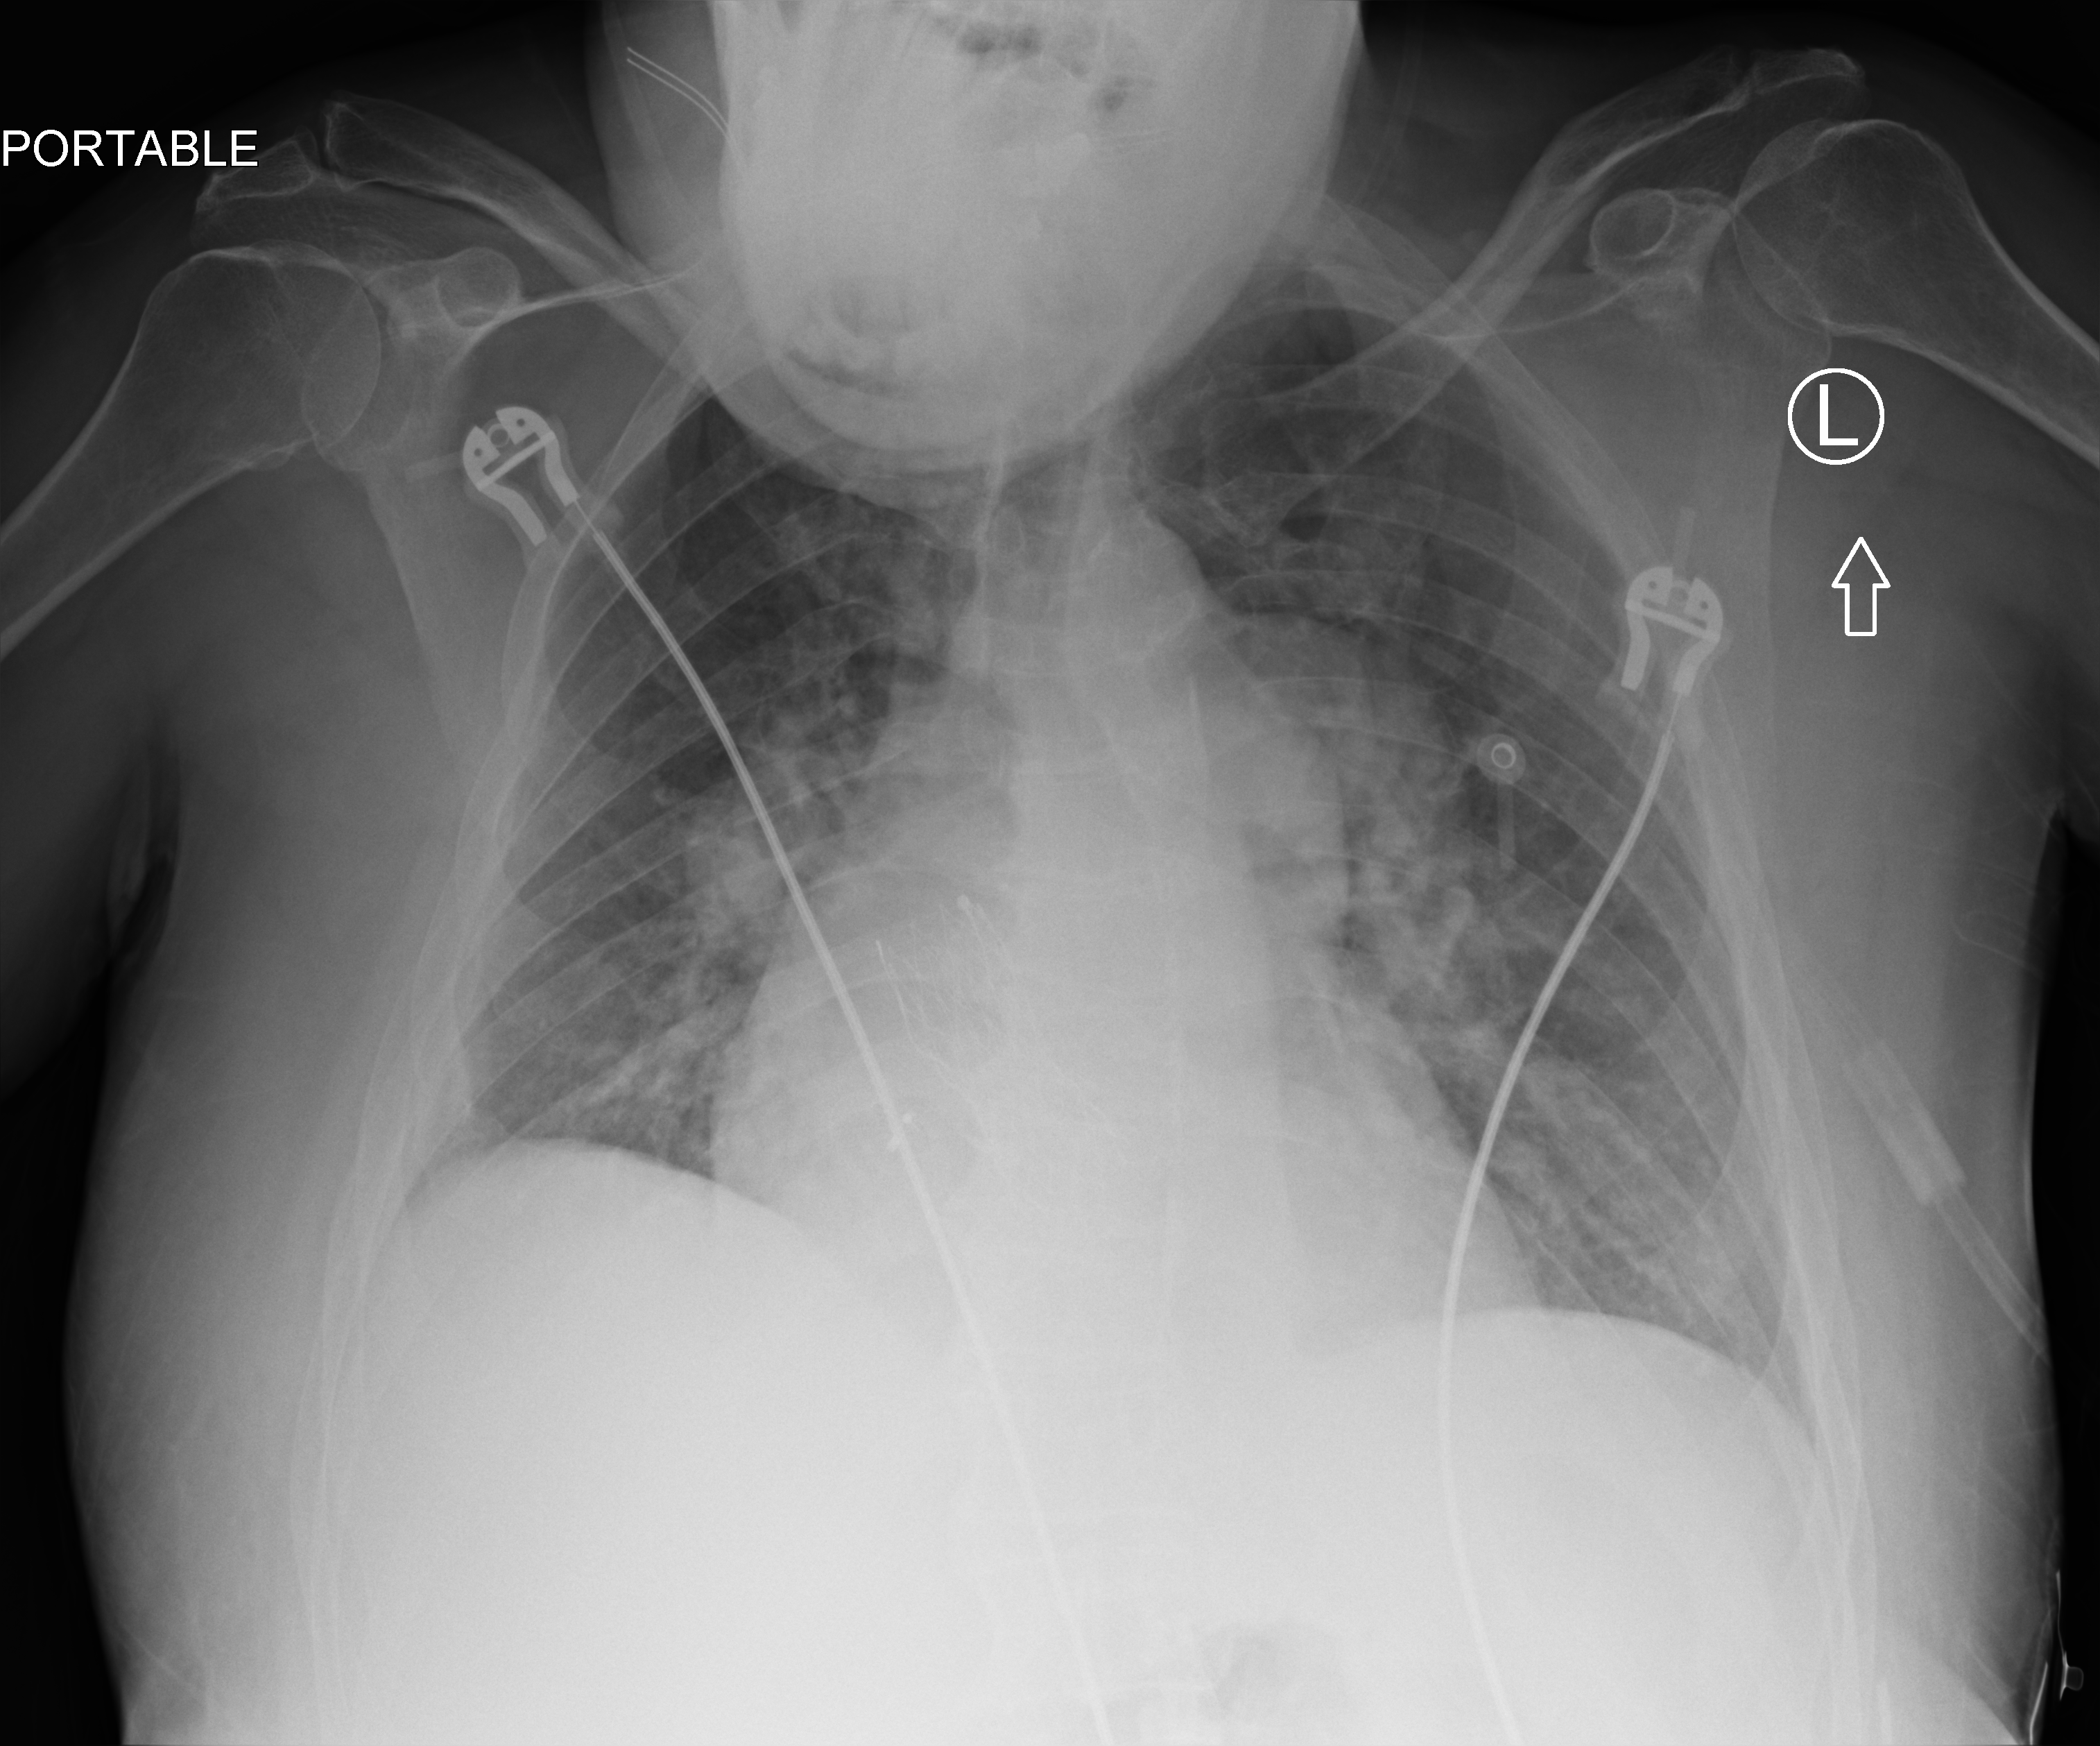
Chest X-ray (portable), anteroposterior (AP) projection. Patient hospitalised with COVID-19; male, aged 60–74 years.
Admission-level facts for this patient (not findings on this image; timing relative to this image not recorded): admitted to intensive care during this hospital stay: no.